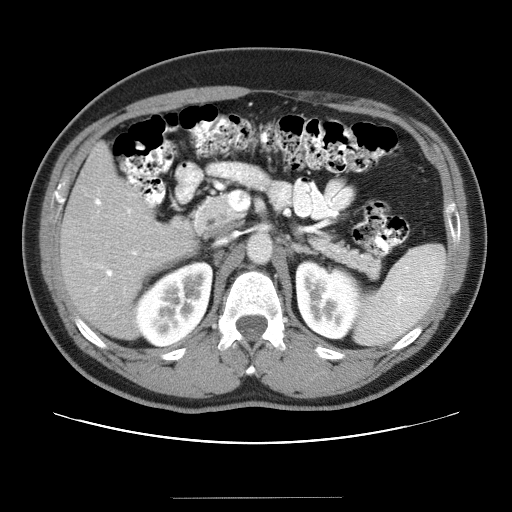
Contrast-enhanced abdominal CT (liver protocol), one axial slice. Reconstruction kernel STANDARD. 120 kVp. Soft-tissue window (W 400 / L 40 HU). 512 × 512 image matrix, field of view 380 × 380 mm. From the clinical record (not read from this slice): diagnosis: hepatocellular carcinoma (patient treated with transarterial chemoembolisation; whether this scan precedes or follows treatment is not stated here); TNM stage (as recorded): Stage-IVA; Child-Pugh class: B.
Outlined on this slice (semi-automatic segmentation, software-assisted and operator-edited):
- liver parenchyma outside the tumour (the mass and vessels are separate outlines, so this box may not span the whole liver): bounding box <60,142,192,338> (left, top, right, bottom; pixels)
- liver vessels: <93,194,148,292>